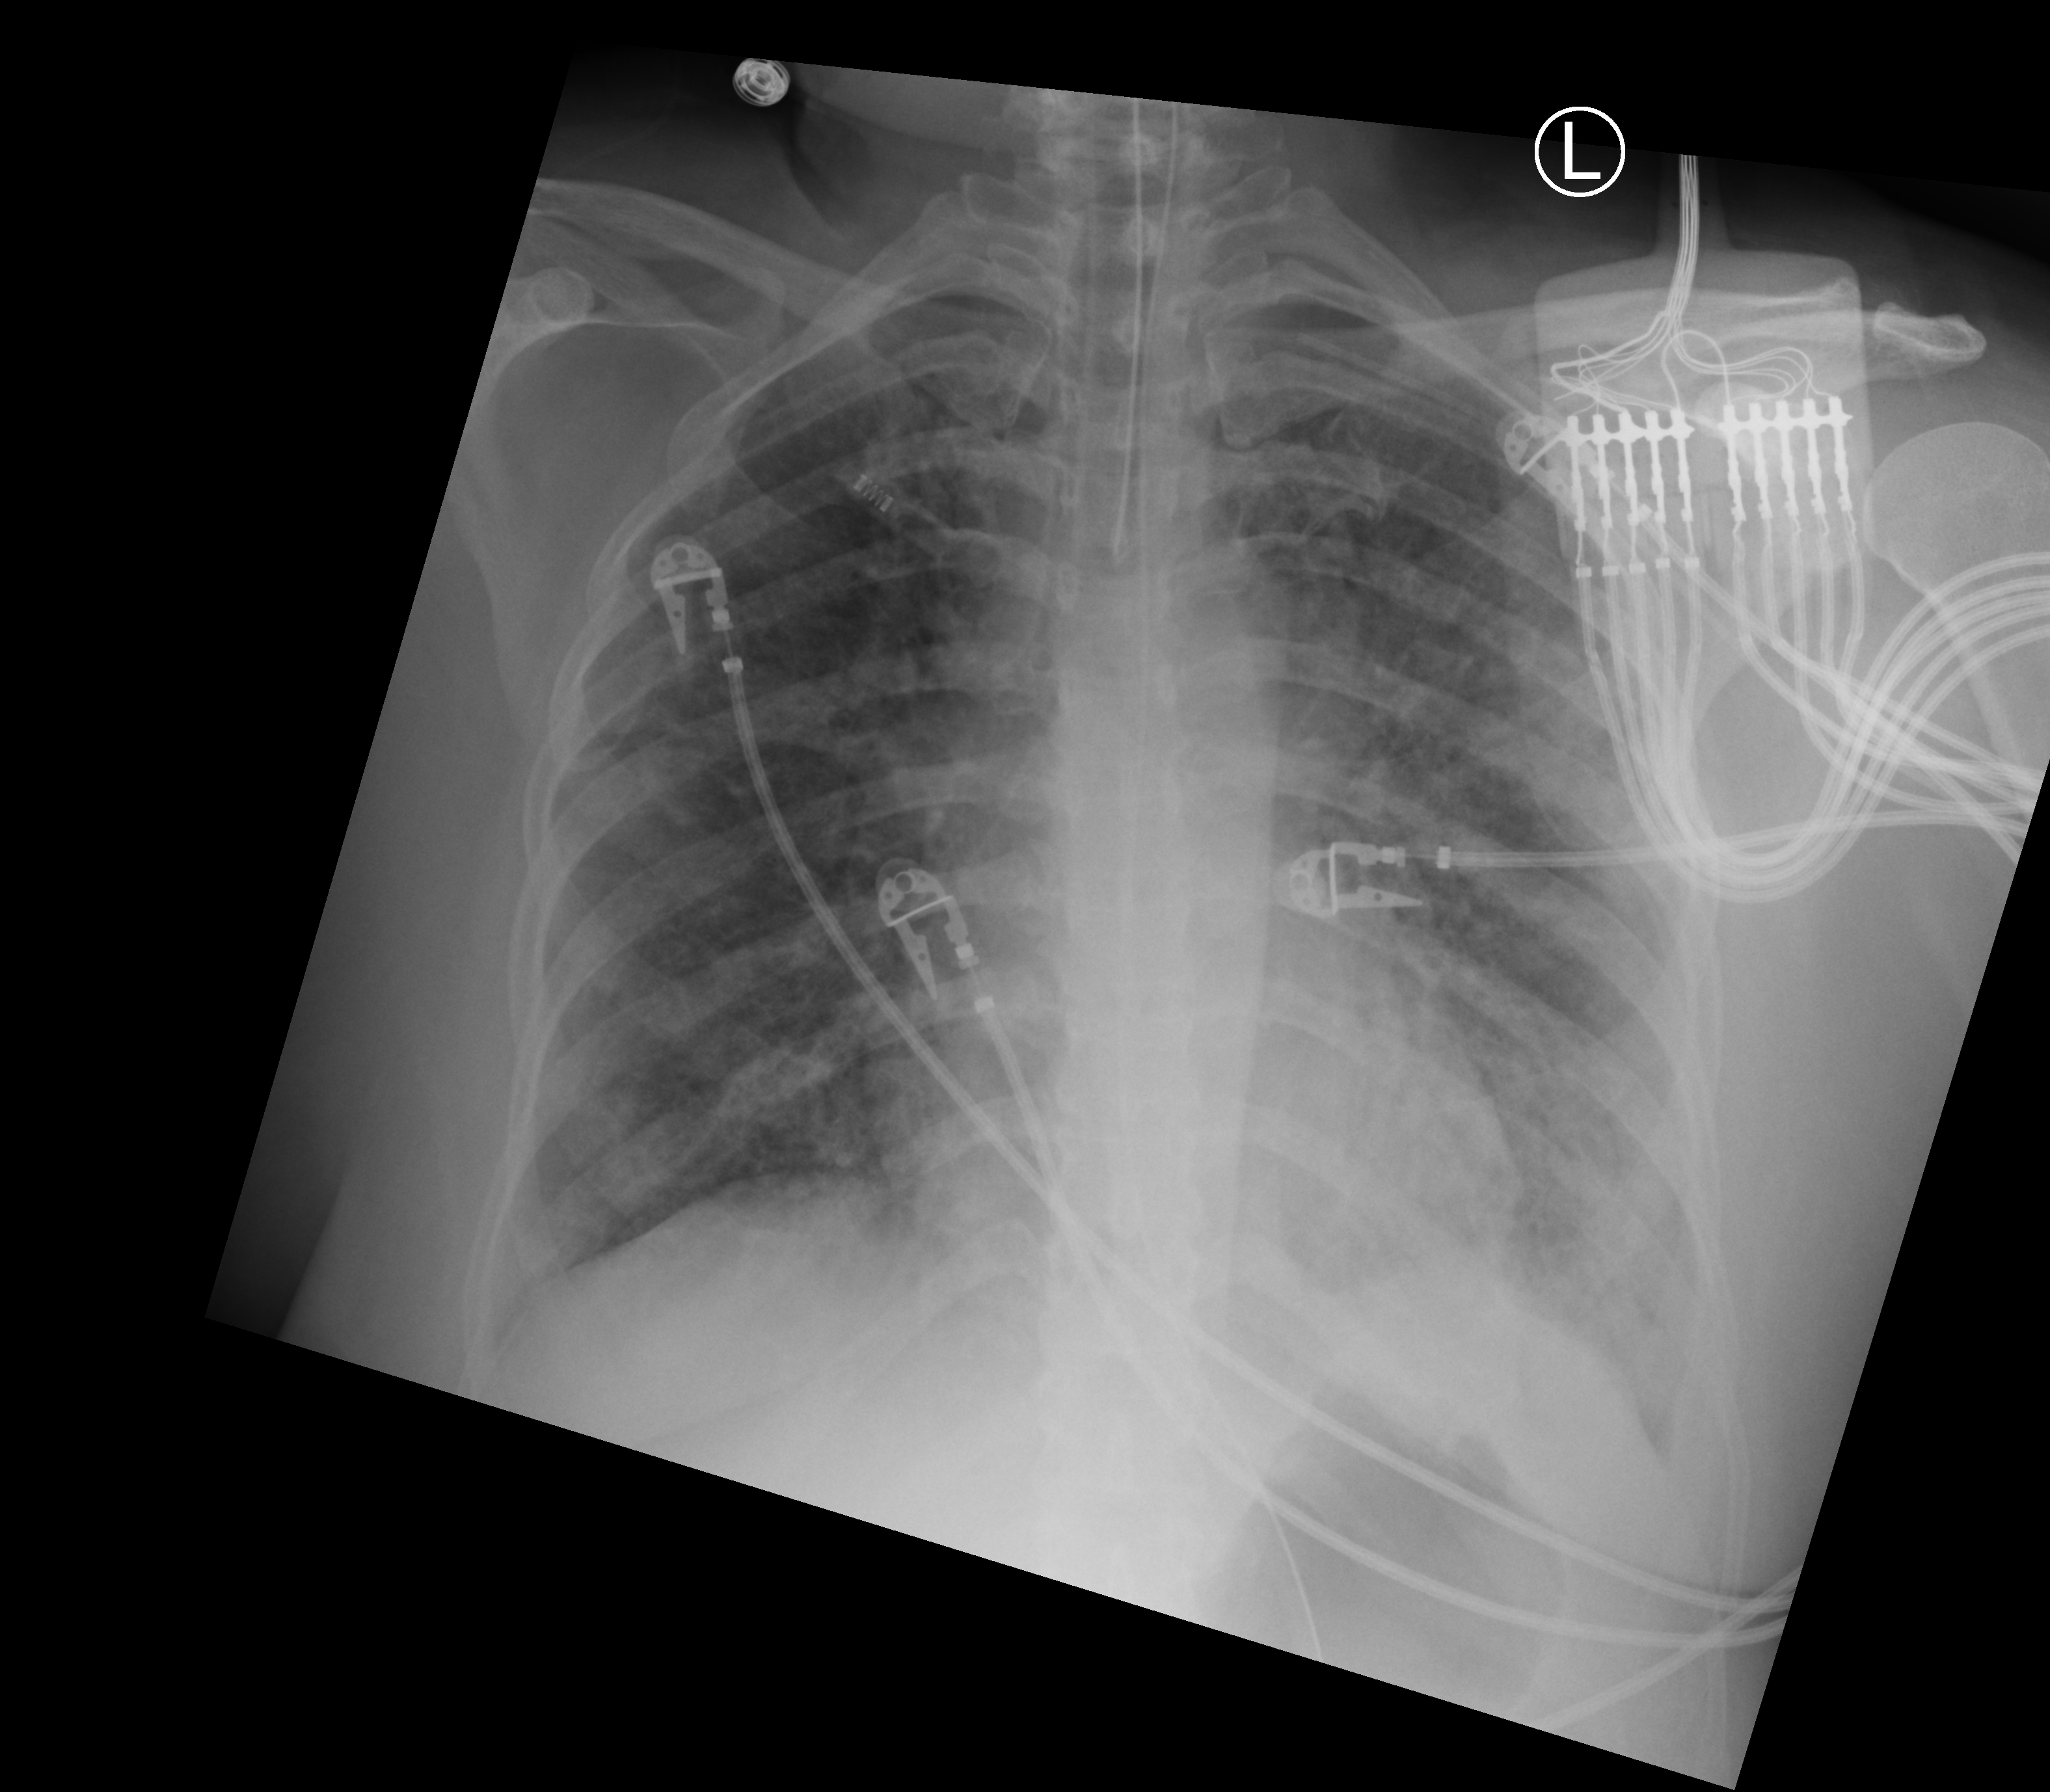
Chest X-ray (portable); anteroposterior (AP) projection. Male patient hospitalised with COVID-19, age 18–59 years.
Admission-level facts for this patient (not findings on this image; timing relative to this image not recorded): COPD (admission record): no; admitted to intensive care during this hospital stay: yes.